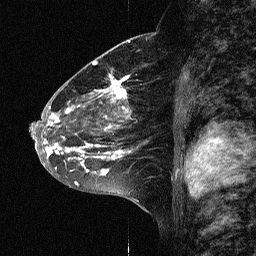
Breast MRI (dynamic contrast-enhanced), one sagittal slice. Slice 34 of 64 in the series (ordered by position). Dynamic contrast-enhanced study with each time point stored as its own series, time point 2 of 3 at this slice position (early post-contrast, ordered by acquisition time). 1.5 T. TE 4.5 ms, TR 11 ms. 256 × 256 image matrix, field of view 200 × 200 mm. Female patient, age 46 years. Case-level facts recorded for this patient, not image findings: setting: breast cancer imaged before/during neoadjuvant chemotherapy; receptor status: HER2-positive.
Annotated regions visible in this slice (semi-automatically segmented with operator editing):
- analysis volume of interest (the breast-tissue region the enhancement analysis was run in; not a lesion): bounding box [x1, y1, x2, y2] px = [43, 72, 166, 177]
- tumour enhancement mask (voxels above the 90 % enhancement threshold inside the analysis volume of interest): [43, 74, 131, 175]